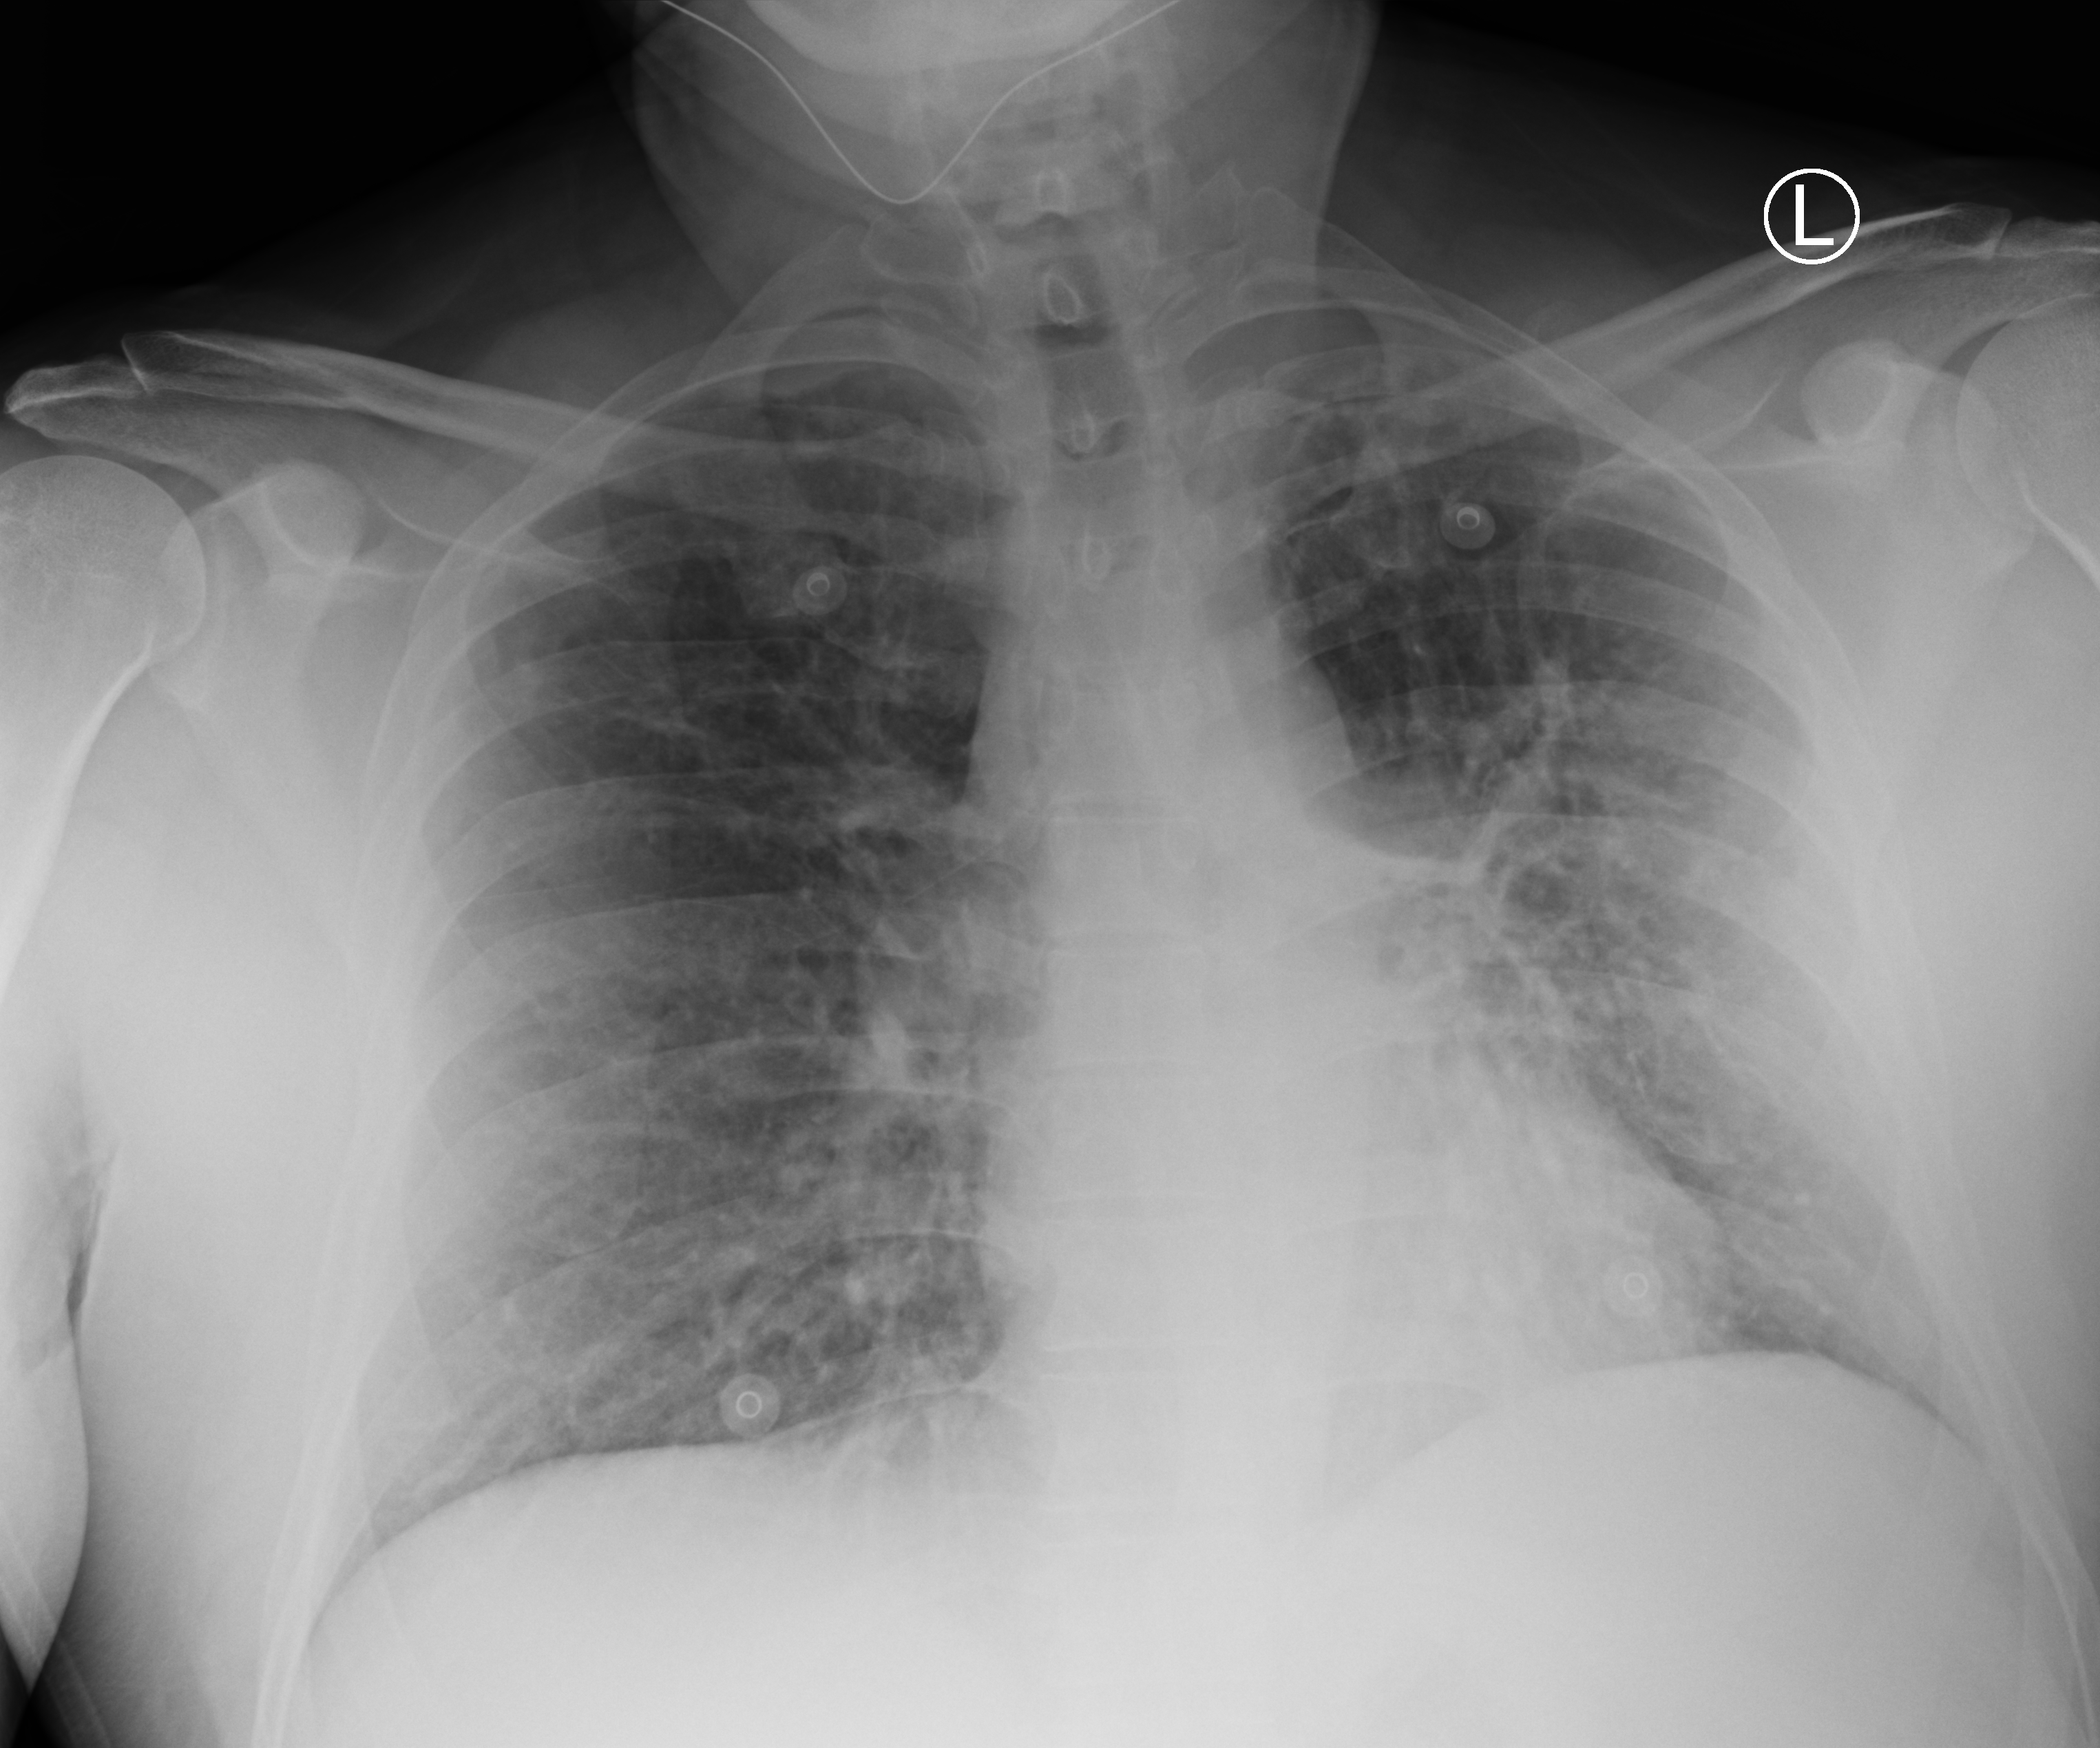
Chest X-ray (portable), anteroposterior (AP) projection. Male patient hospitalised with COVID-19, age 18–59 years.
Admission-level facts for this patient (not findings on this image; timing relative to this image not recorded): mechanically ventilated during this hospital stay: no; length of hospital stay: 2 days; diabetes (admission record): no.